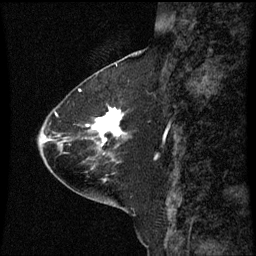
Breast MRI (dynamic contrast-enhanced), one sagittal slice; position 24 of 60 along the scan axis; dynamic contrast-enhanced series, image 2 of 3 at this slice position (ordered by acquisition); 1.5 T; TE 4.2 ms, TR 8.9 ms; 2 mm slice thickness; 256 × 256 image matrix, field of view 200 × 200 mm. Patient: female, 63 years. Case-level facts recorded for this patient, not image findings: setting: breast cancer imaged before/during neoadjuvant chemotherapy; receptor status: HR-positive, HER2-negative.
Structures marked on this image (semi-automatically segmented with operator editing):
- analysis volume of interest (the breast-tissue region the enhancement analysis was run in; not a lesion): box from (x=87, y=104) to (x=127, y=151) px
- tumour enhancement mask (voxels above the 70 % enhancement threshold inside the analysis volume of interest): (x=92, y=108)–(x=122, y=147)